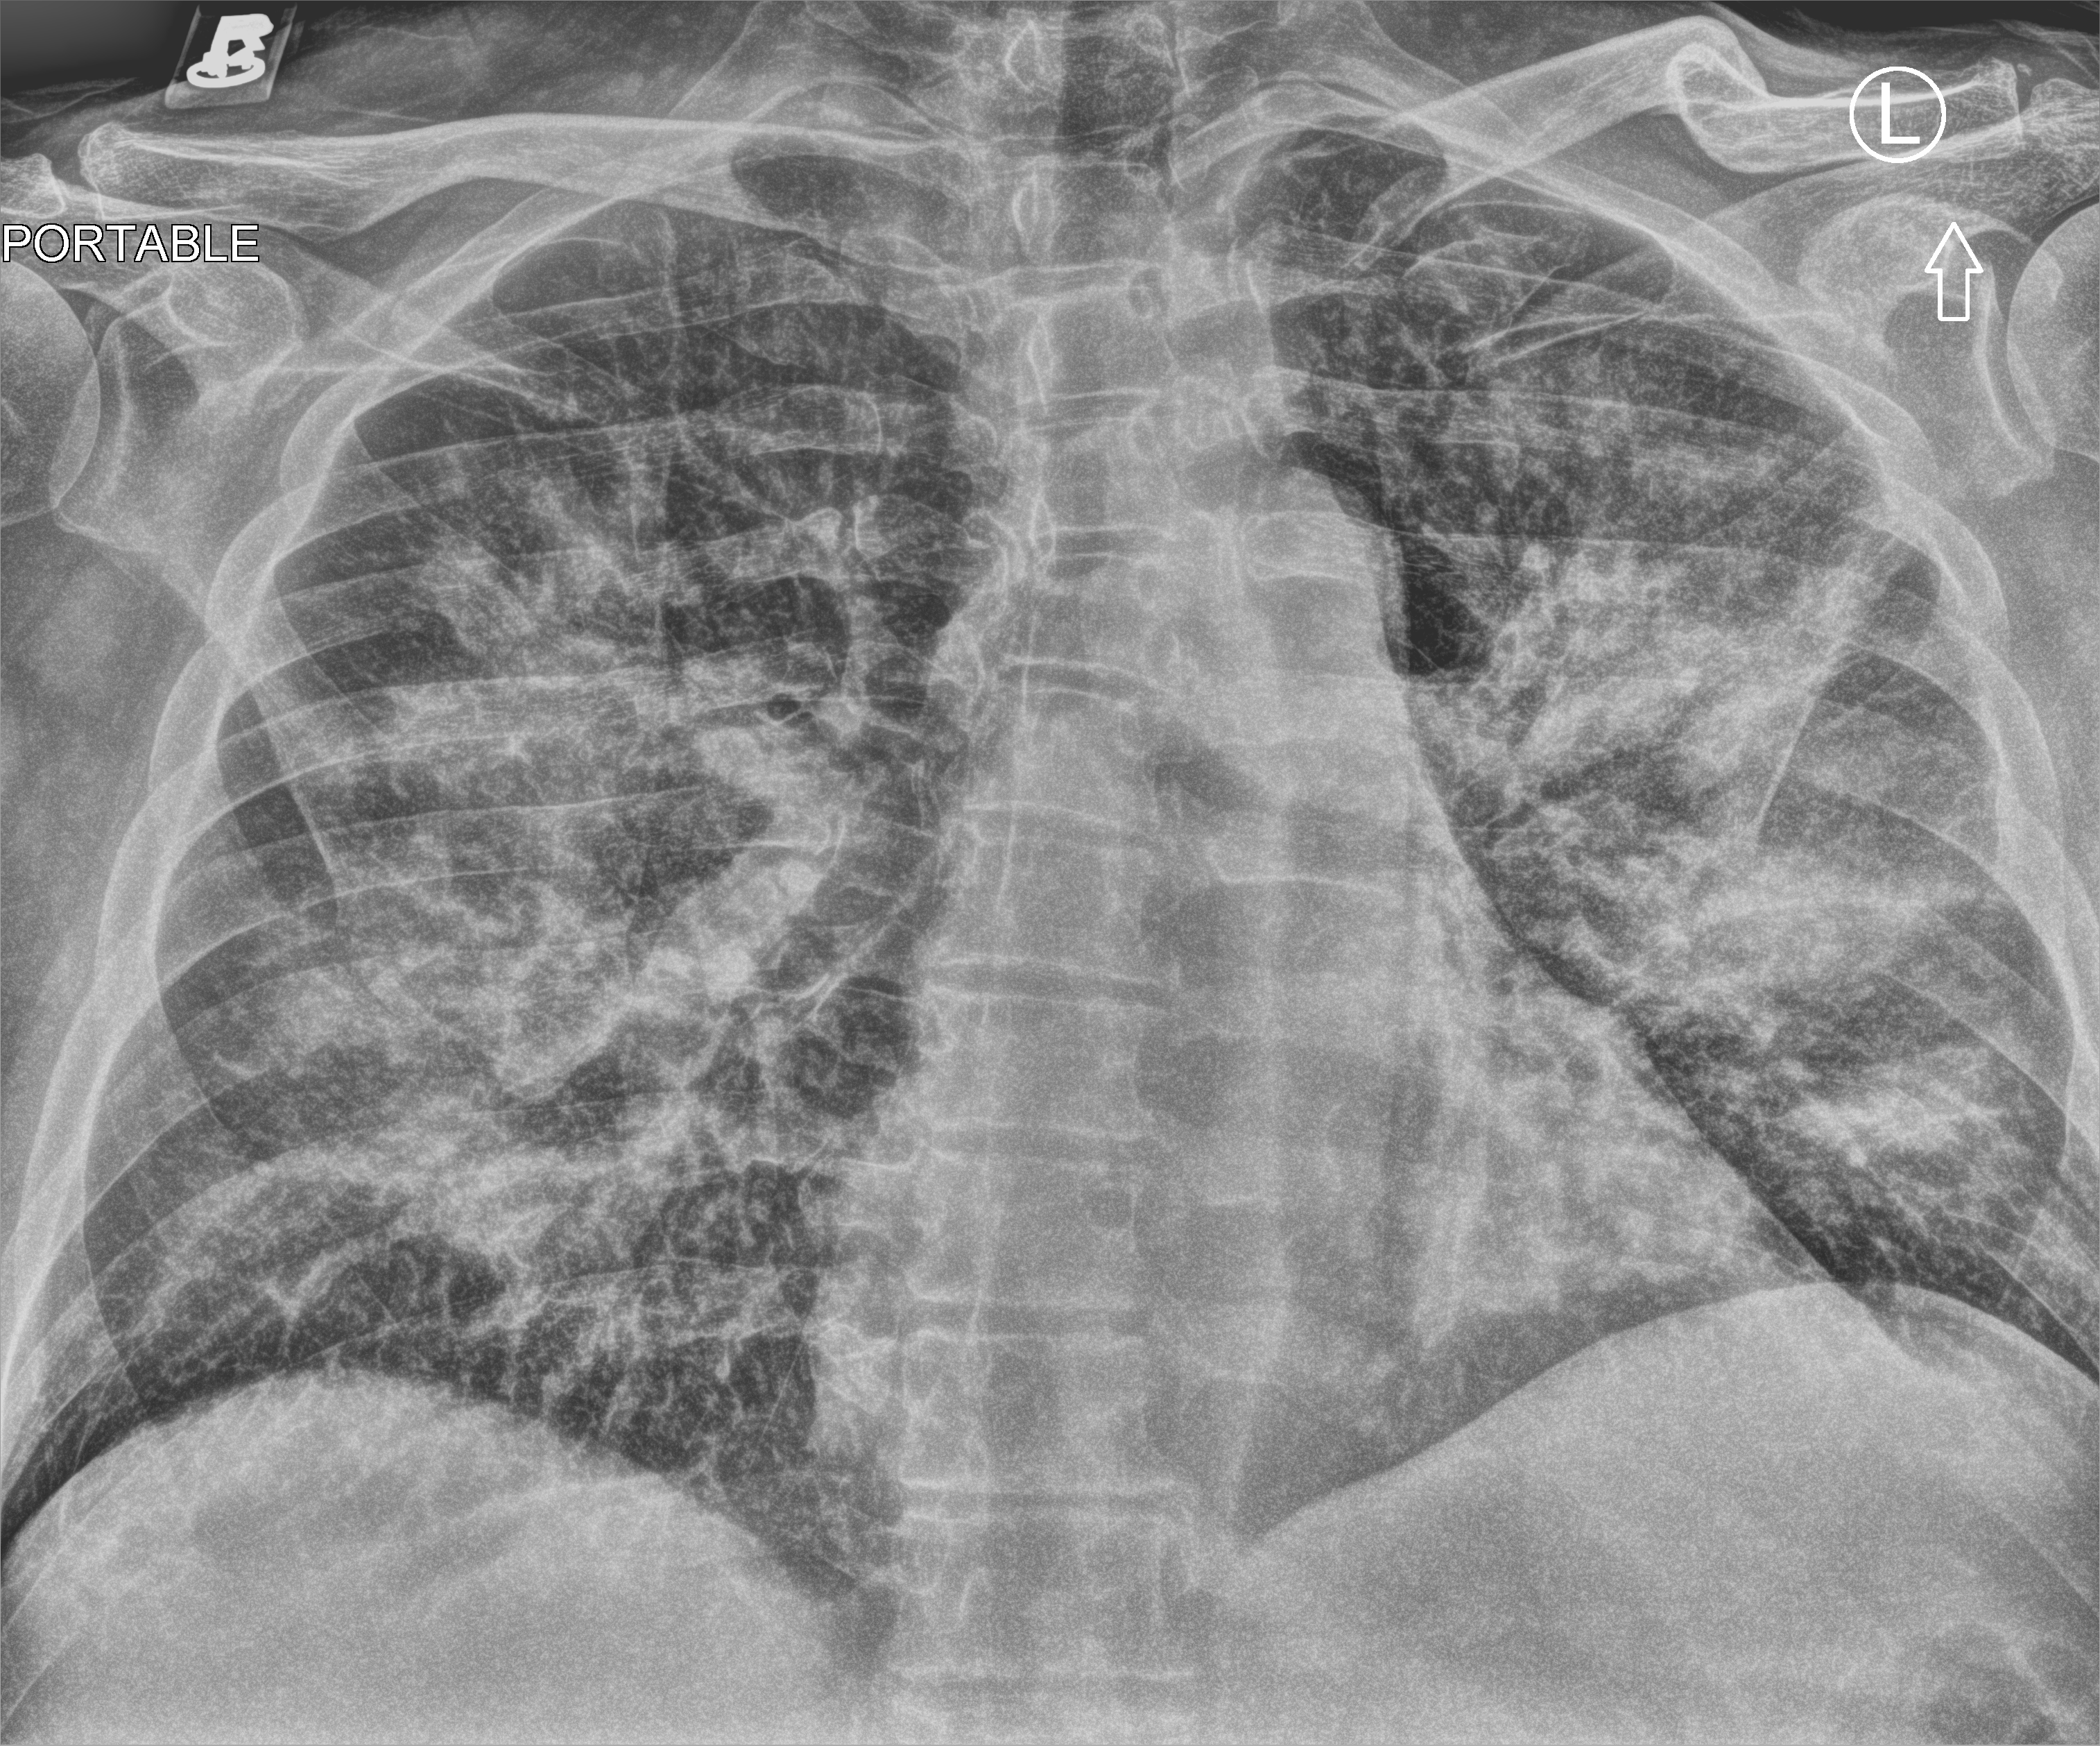
Chest X-ray (portable), anteroposterior (AP) projection. Patient hospitalised with COVID-19; male, aged 60–74 years.
From the hospital-stay record, not from the radiograph (when in the stay this image was taken is not recorded): hypertension (admission record): yes; admitted to intensive care during this hospital stay: no.